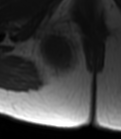
MRI of an extremity soft-tissue mass, one axial slice. Slice 28 of 47 in the series (ordered by position). MR volume resampled by the dataset authors to the PET/CT grid (not the native acquisition matrix). 3.27 mm slice thickness. 121 × 139 image matrix, field of view 118 × 136 mm. Female patient. From the clinical record (not read from this slice): histological type: epithelioid sarcoma; grade: intermediate; site of the primary tumour: right buttock.
Outlined on this slice (expert contour drawn on MRI and transferred to this co-registered scan by the dataset authors):
- gross tumour volume including surrounding oedema: bounding box <34,25,81,81> (left, top, right, bottom; pixels)
- gross tumour volume (mass): <38,34,74,76>